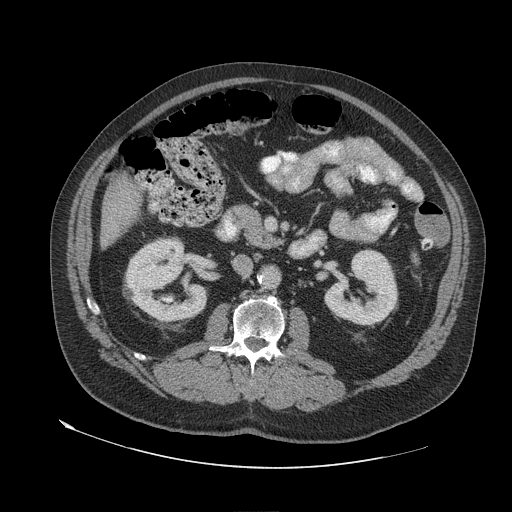
Contrast-enhanced abdominal CT (liver protocol), one axial slice; slice 15 of 79 in the series (ordered by position); reconstruction kernel STANDARD; soft-tissue window (W 400 / L 40 HU); 512 × 512 image matrix, field of view 480 × 480 mm. Case-level facts recorded for this patient, not image findings: diagnosis: hepatocellular carcinoma (patient treated with transarterial chemoembolisation; whether this scan precedes or follows treatment is not stated here); TNM stage (as recorded): Stage-IVA; Child-Pugh class: A; tumour differentiation: well differentiated; tumour nodularity: multinodular.
Outlined on this slice (semi-automatic segmentation, software-assisted and operator-edited):
- liver parenchyma outside the tumour (the mass and vessels are separate outlines, so this box may not span the whole liver): bounding box (x1, y1, x2, y2) in pixels: (100, 176, 140, 248)